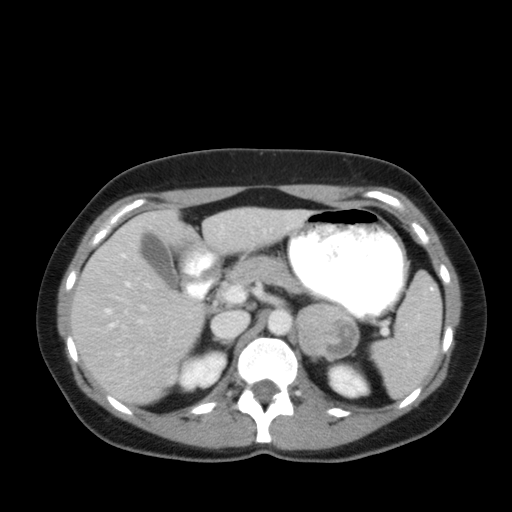
Contrast-enhanced abdominal CT, one axial slice; position 34 of 92 along the scan axis; intravenous contrast given; soft-tissue window (W 400 / L 40 HU); 5 mm slice thickness; 512 × 512 image matrix, field of view 369 × 369 mm. Female patient, age 35 years. From the clinical record (not read from this slice): diagnosis: adrenocortical carcinoma; tumour side: left adrenal; tumour size at pathology: 6.6 cm; Ki-67 index: 5 %; stage (as recorded): 2.
Structures marked on this image (semi-automatic segmentation, software-assisted and operator-edited):
- mass: bounding box <297,304,357,360> (left, top, right, bottom; pixels)